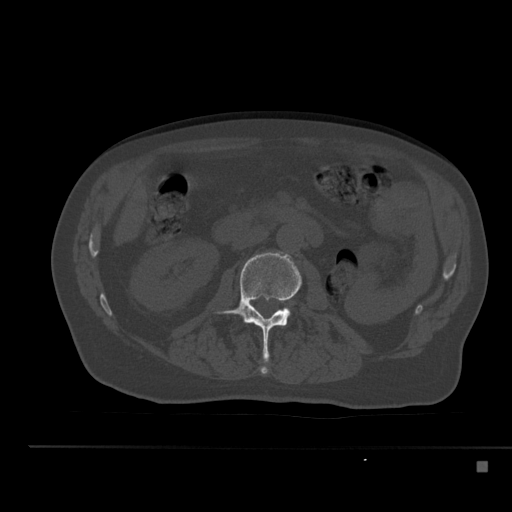
CT including the spine, one axial slice; slice 184 of 517 in the series (ordered by position); bone window (W 1800 / L 400 HU); 512 × 512 image matrix, field of view 408 × 408 mm. Male patient, age 70 years. Case-level facts recorded for this patient, not image findings: primary cancer: renal; vertebrae with lytic lesions (as recorded): T4, T6, T10, T12, L3, L4, L5.
Annotated regions visible in this slice (semi-automatically segmented with operator editing):
- L2 vertebra: bounding box [x1, y1, x2, y2] px = [215, 252, 302, 374]